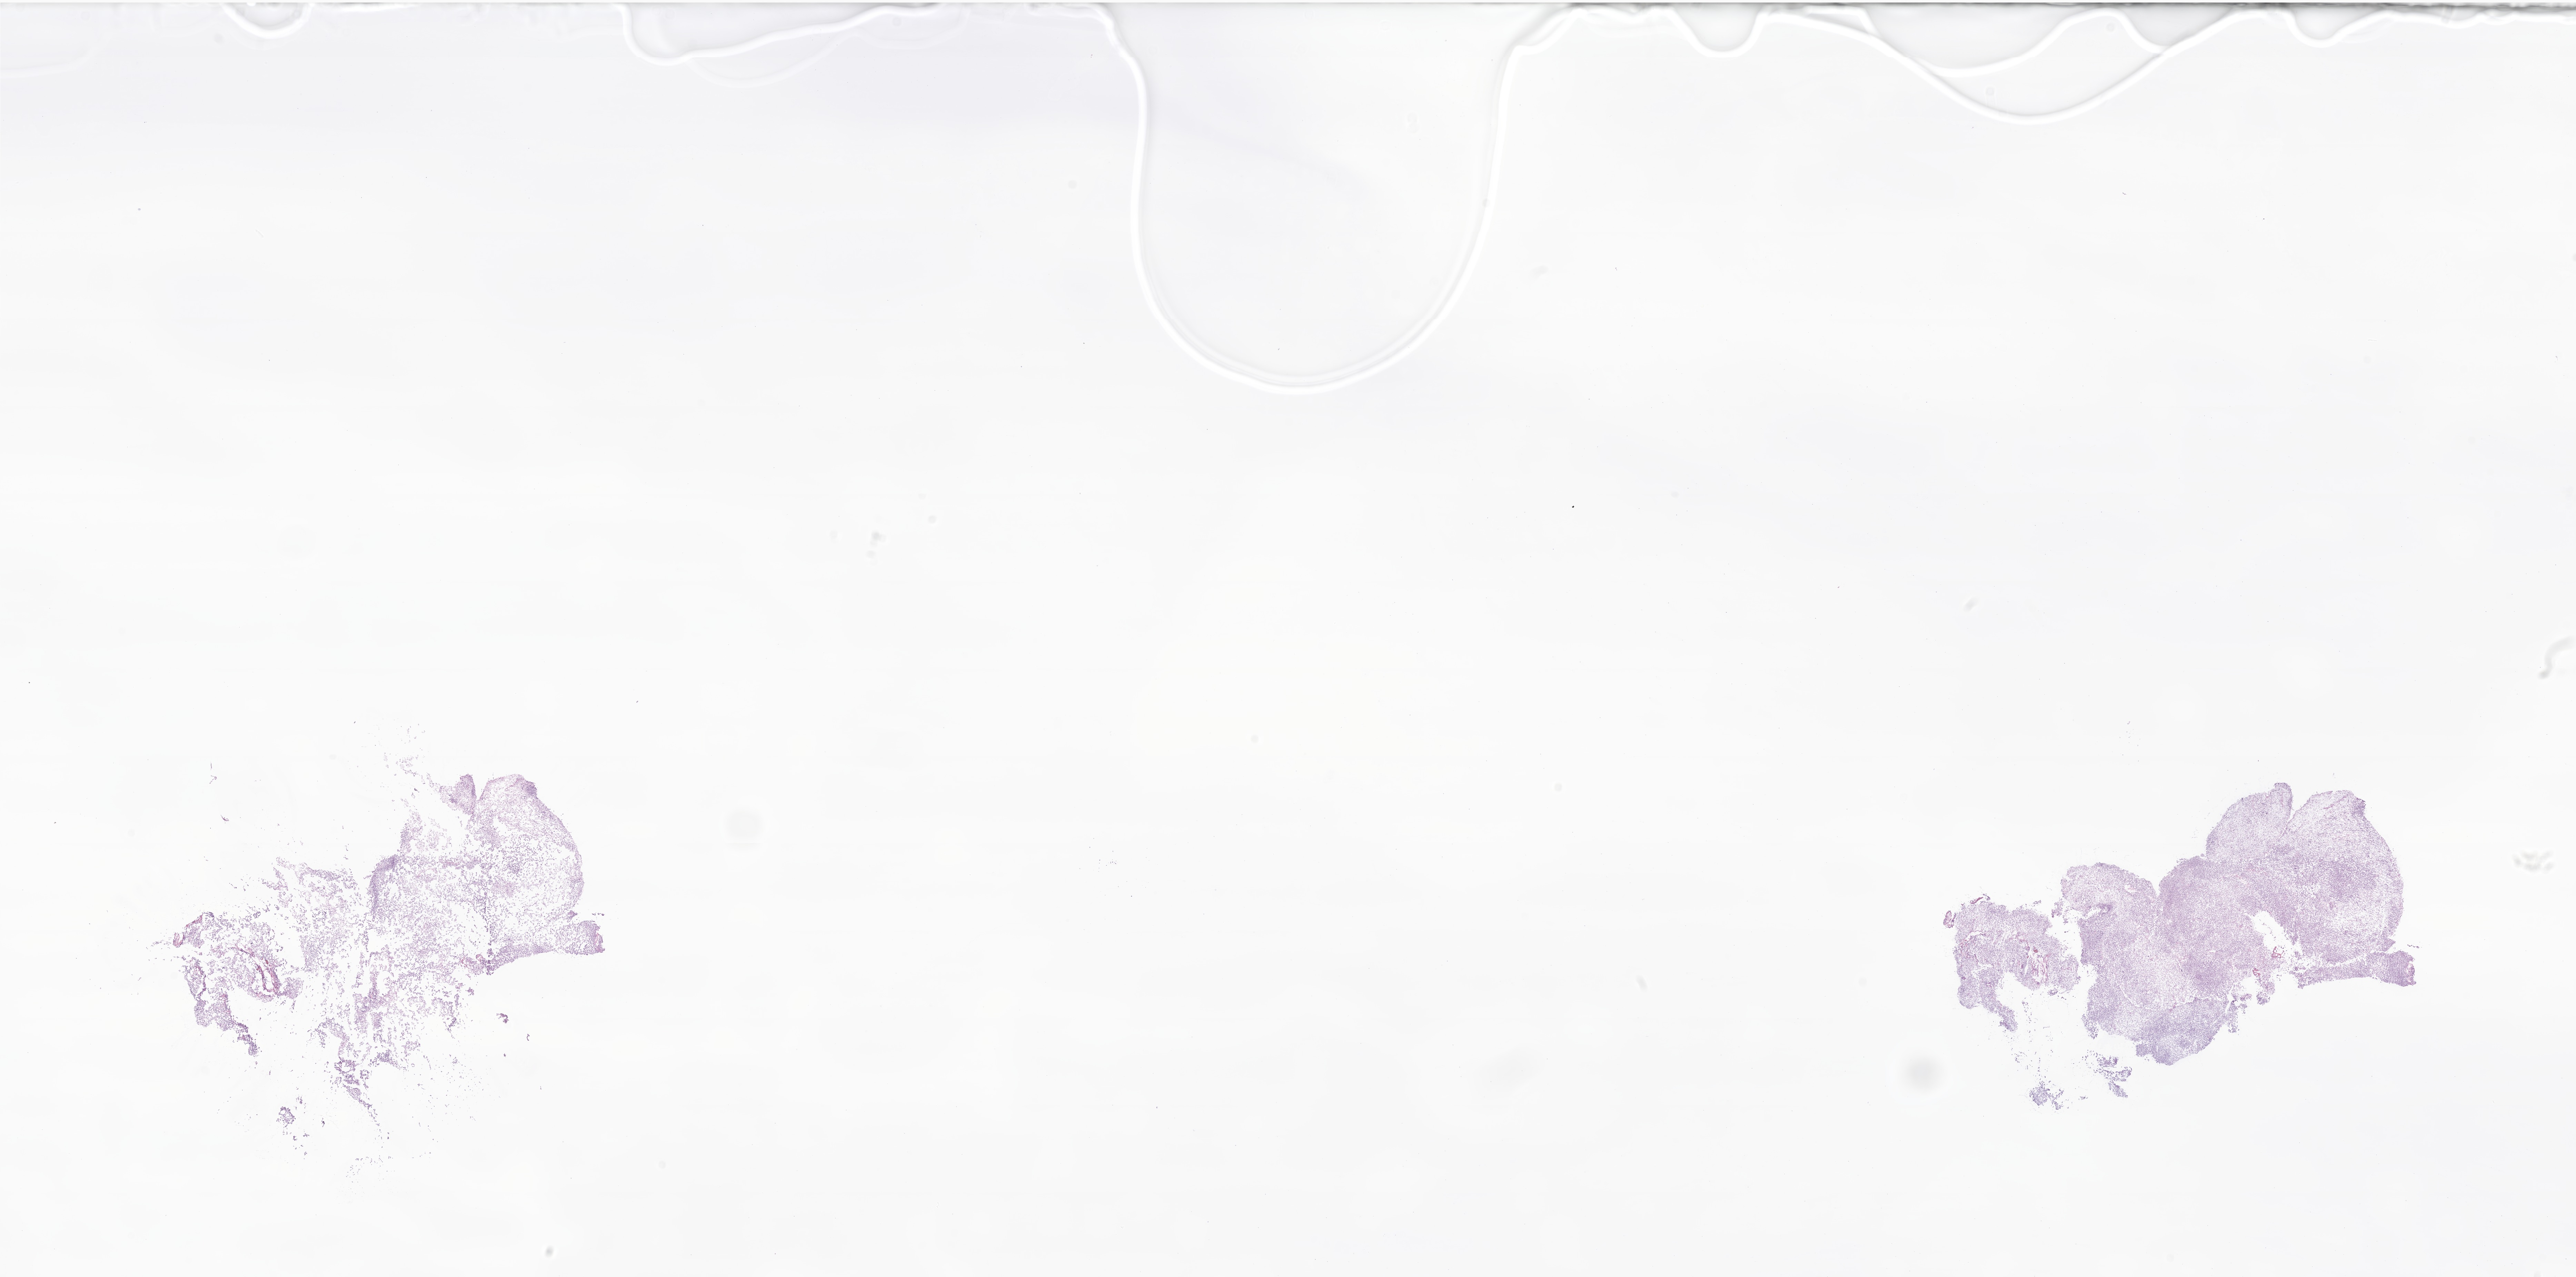
Haematoxylin and eosin whole-slide image of tumor tissue from the mediastinum, shown as a low-resolution overview of the whole scanned area (about 31.5 x 15.6 mm). Frozen section (OCT-embedded). Patient: female, age 42 months.
* diagnosis: Neoplasm, malignant